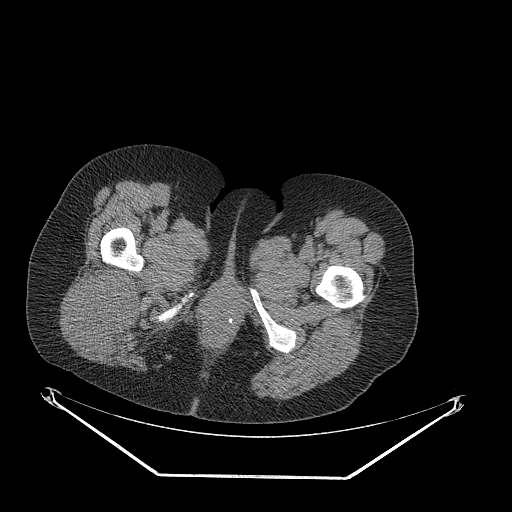
CT of an extremity soft-tissue mass (from a PET/CT study), one axial slice. Position 54 of 257 along the scan axis. Reconstruction kernel STANDARD. 140 kVp. Soft-tissue window (W 400 / L 40 HU). 3.75 mm slice thickness. 512 × 512 image matrix. Female patient. Case-level facts recorded for this patient, not image findings: histological type: synovial sarcoma; grade: intermediate; site of the primary tumour: right buttock.
Structures marked on this image (expert contour drawn on MRI and transferred to this co-registered scan by the dataset authors):
- gross tumour volume including surrounding oedema: bounding box <73,265,143,353> (left, top, right, bottom; pixels)
- gross tumour volume (mass): <73,265,143,346>